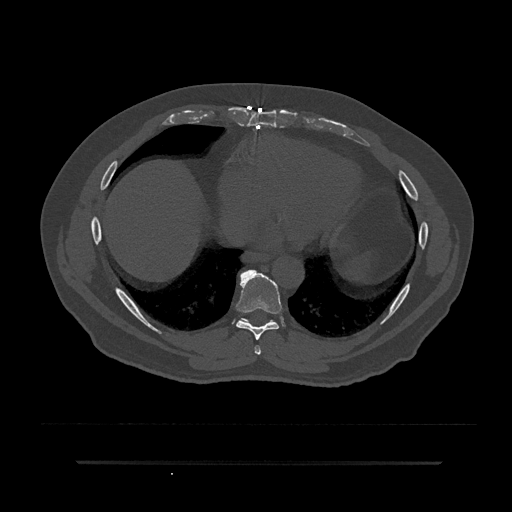
CT including the spine, one axial slice; slice 418 of 797 in the series (ordered by position); reconstruction kernel Br40s/3; 120 kVp; bone window (W 1800 / L 400 HU); 0.5 mm slice thickness; 512 × 512 image matrix, field of view 464 × 464 mm. Male patient, age 59 years. From the clinical record (not read from this slice): primary cancer: bile ducts.
Structures marked on this image (semi-automatic segmentation, software-assisted and operator-edited):
- T7 vertebra: box from (x=254, y=345) to (x=261, y=355) px
- T8 vertebra: (x=236, y=269)–(x=282, y=340)
- T9 vertebra: (x=242, y=318)–(x=273, y=321)